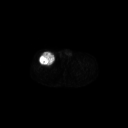
FDG PET of an extremity soft-tissue mass (from a PET/CT study), one axial slice. Position 288 of 311 along the scan axis. 3.27 mm slice thickness. 128 × 128 image matrix. Male patient, age 56 years. From the clinical record (not read from this slice): histological type: pleiomorphic leiomyosarcoma; grade: intermediate; site of the primary tumour: right thigh.
Structures marked on this image (expert contour drawn on MRI and transferred to this co-registered scan by the dataset authors):
- gross tumour volume including surrounding oedema: bounding box (x1, y1, x2, y2) in pixels: (38, 52, 55, 66)
- gross tumour volume (mass): (38, 52, 55, 66)